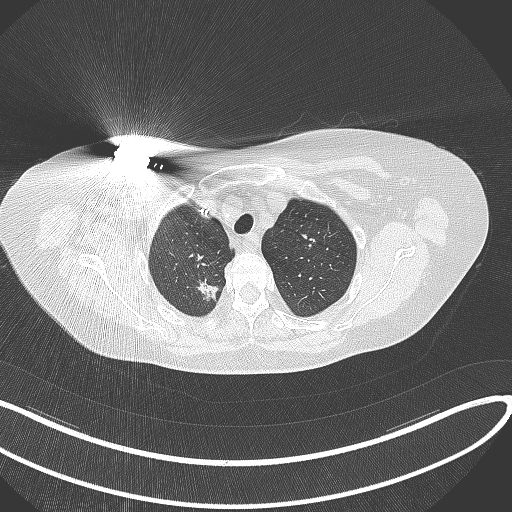
Chest CT, one axial slice; slice 278 of 316 in the series (ordered by position); lung window (W 1500 / L -600 HU); 512 × 512 image matrix. Patient: female, 72 years. From the clinical record (not read from this slice): clinical TNM (as recorded): T1c N0 M0.
Outlined on this slice (bounding box drawn by a radiologist):
- lung tumour (recorded histology: adenocarcinoma): bounding box (x1, y1, x2, y2) in pixels: (188, 278, 221, 303)